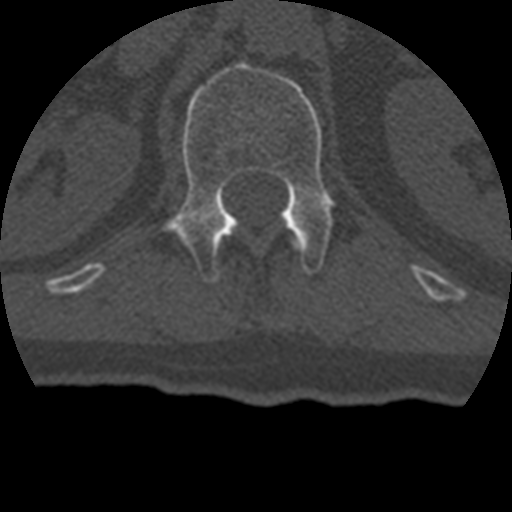
CT including the spine, one axial slice. Position 152 of 399 along the scan axis. Bone window (W 1800 / L 400 HU). 1.25 mm slice thickness. 512 × 512 image matrix, field of view 160 × 160 mm. Patient age 69 years. From the clinical record (not read from this slice): primary cancer: prostate.
Structures marked on this image (semi-automatically segmented with operator editing):
- L1 vertebra: bounding box <164,62,335,282> (left, top, right, bottom; pixels)